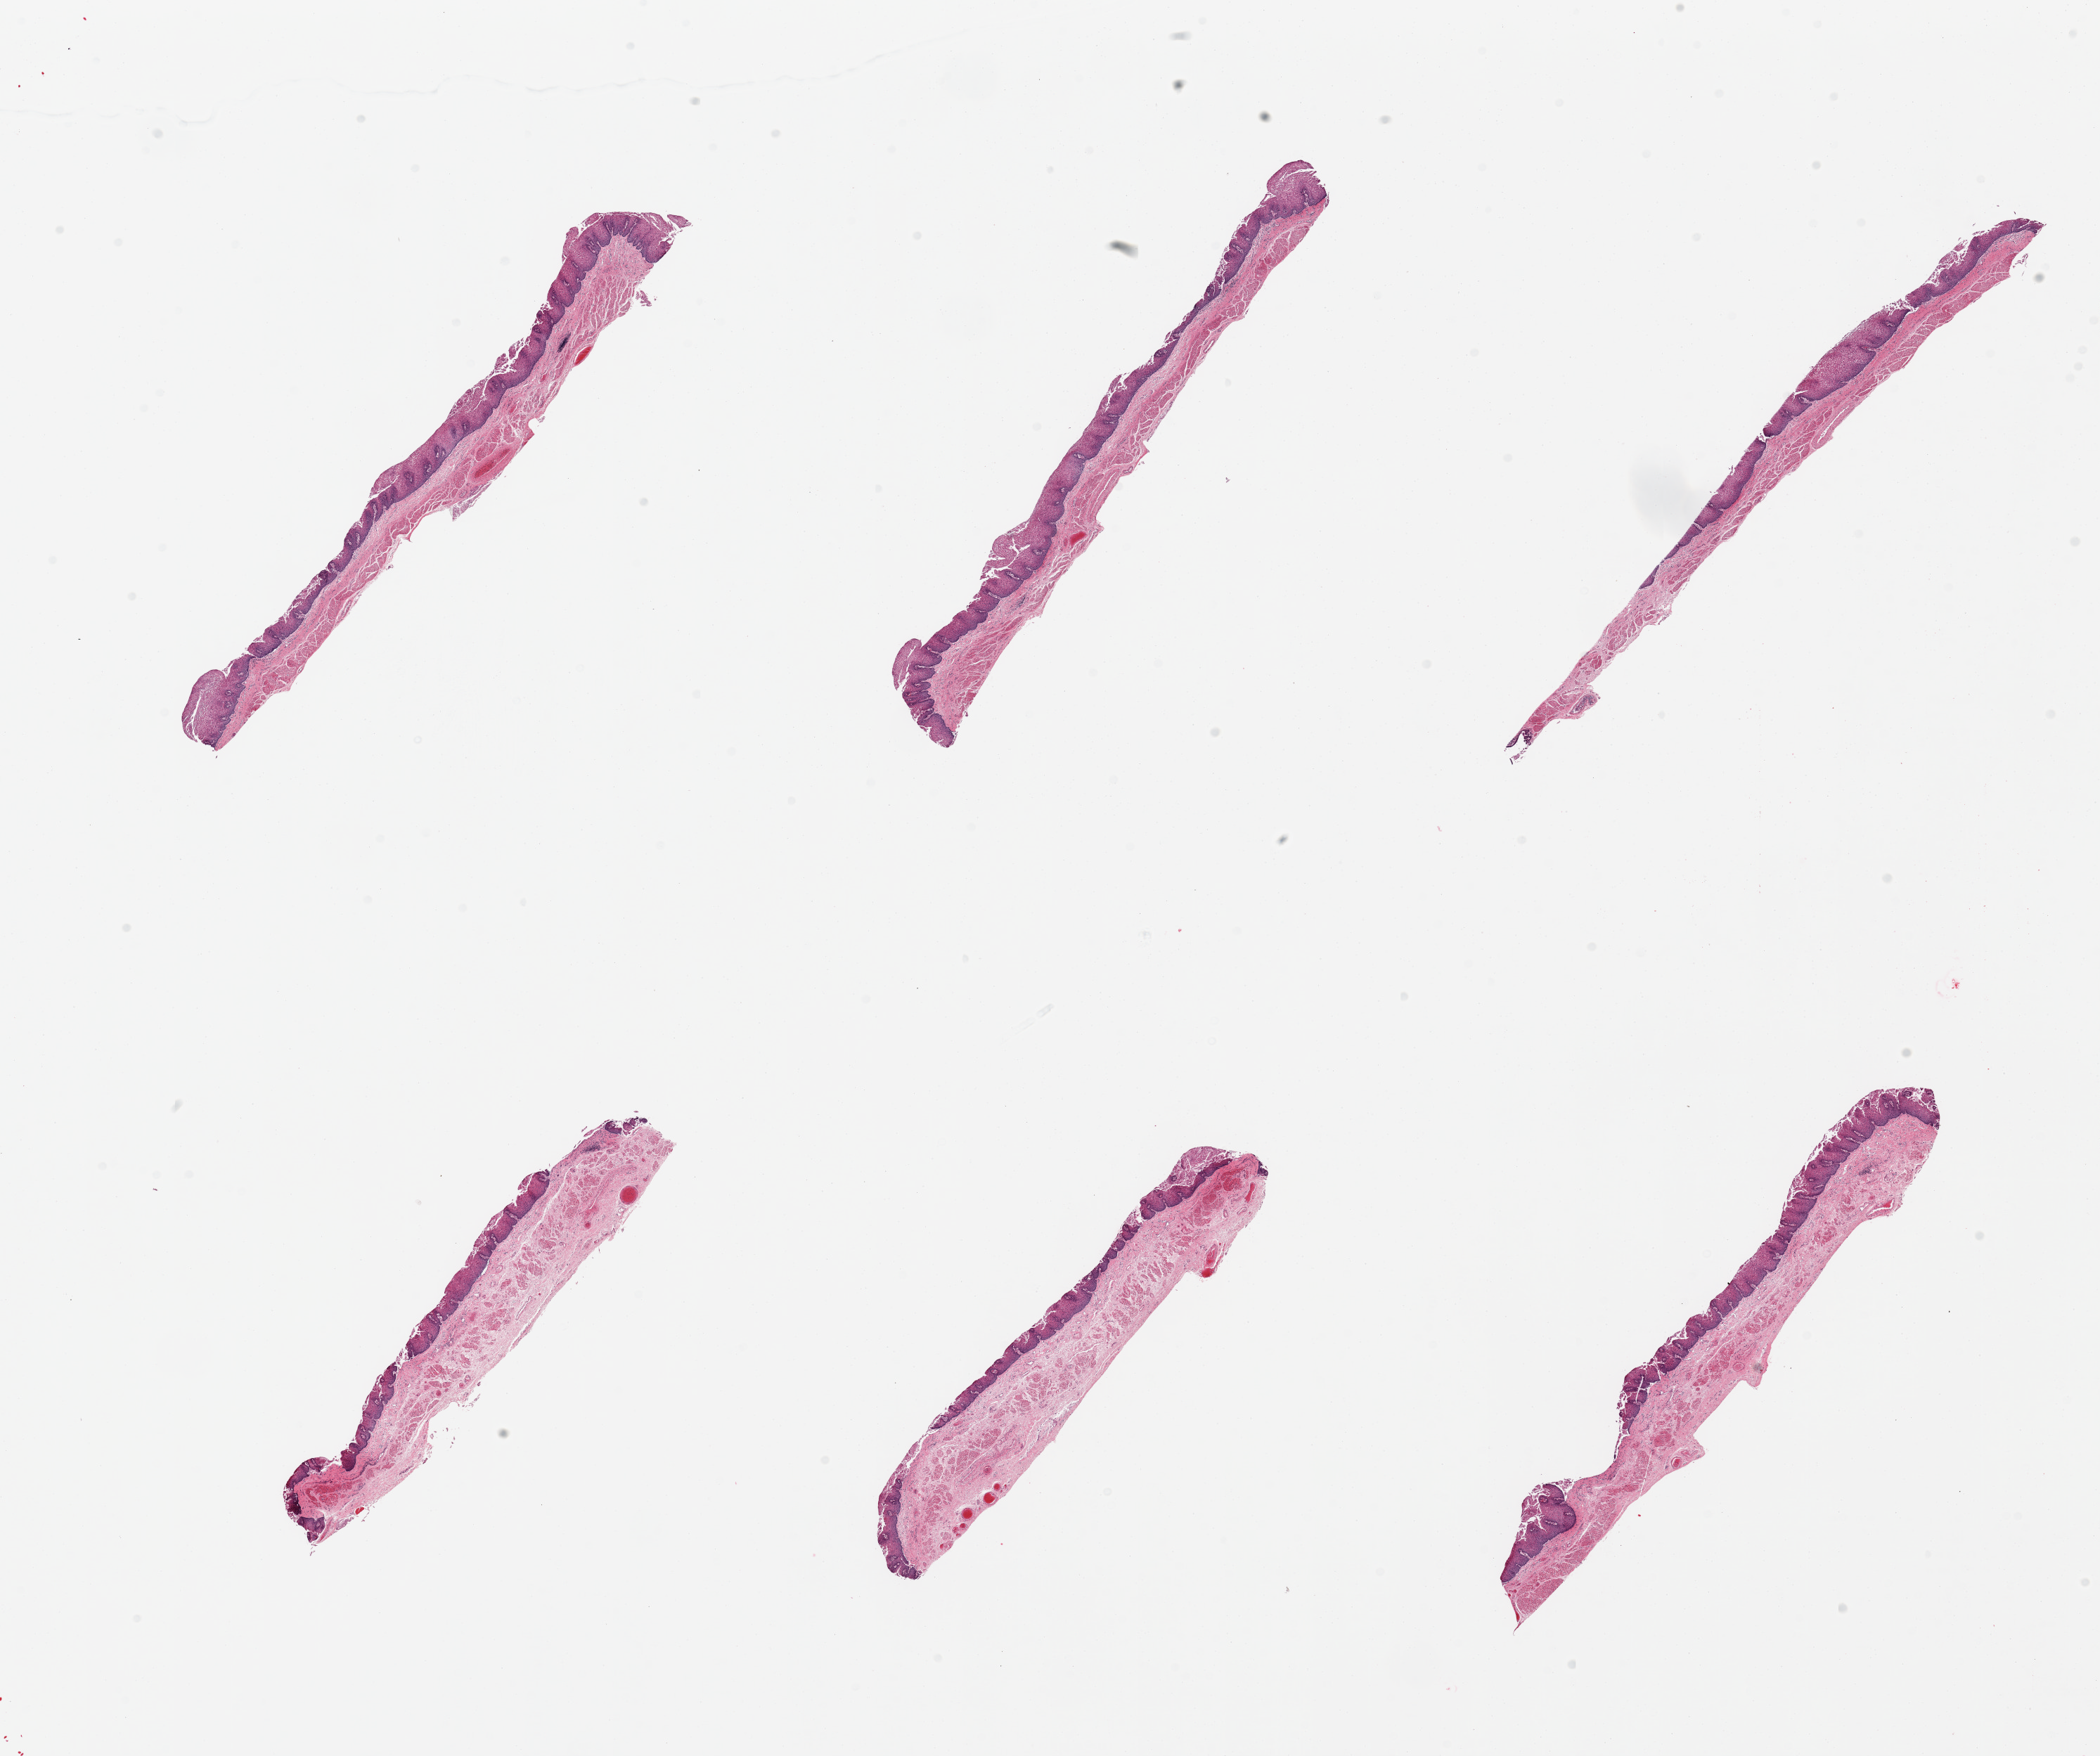
Digitized H&E-stained section, brightfield, low-resolution overview of the scanned area, about 23.6 x 19.8 mm. PAXgene-fixed paraffin-embedded (PFPE) section. Section of esophageal mucous membrane (target tissue). Tissue donor sample.
Pathologist's review note for this sample: 6 pieces, squmaous mucosa up to ~0.25mm, 40-50% thickness.